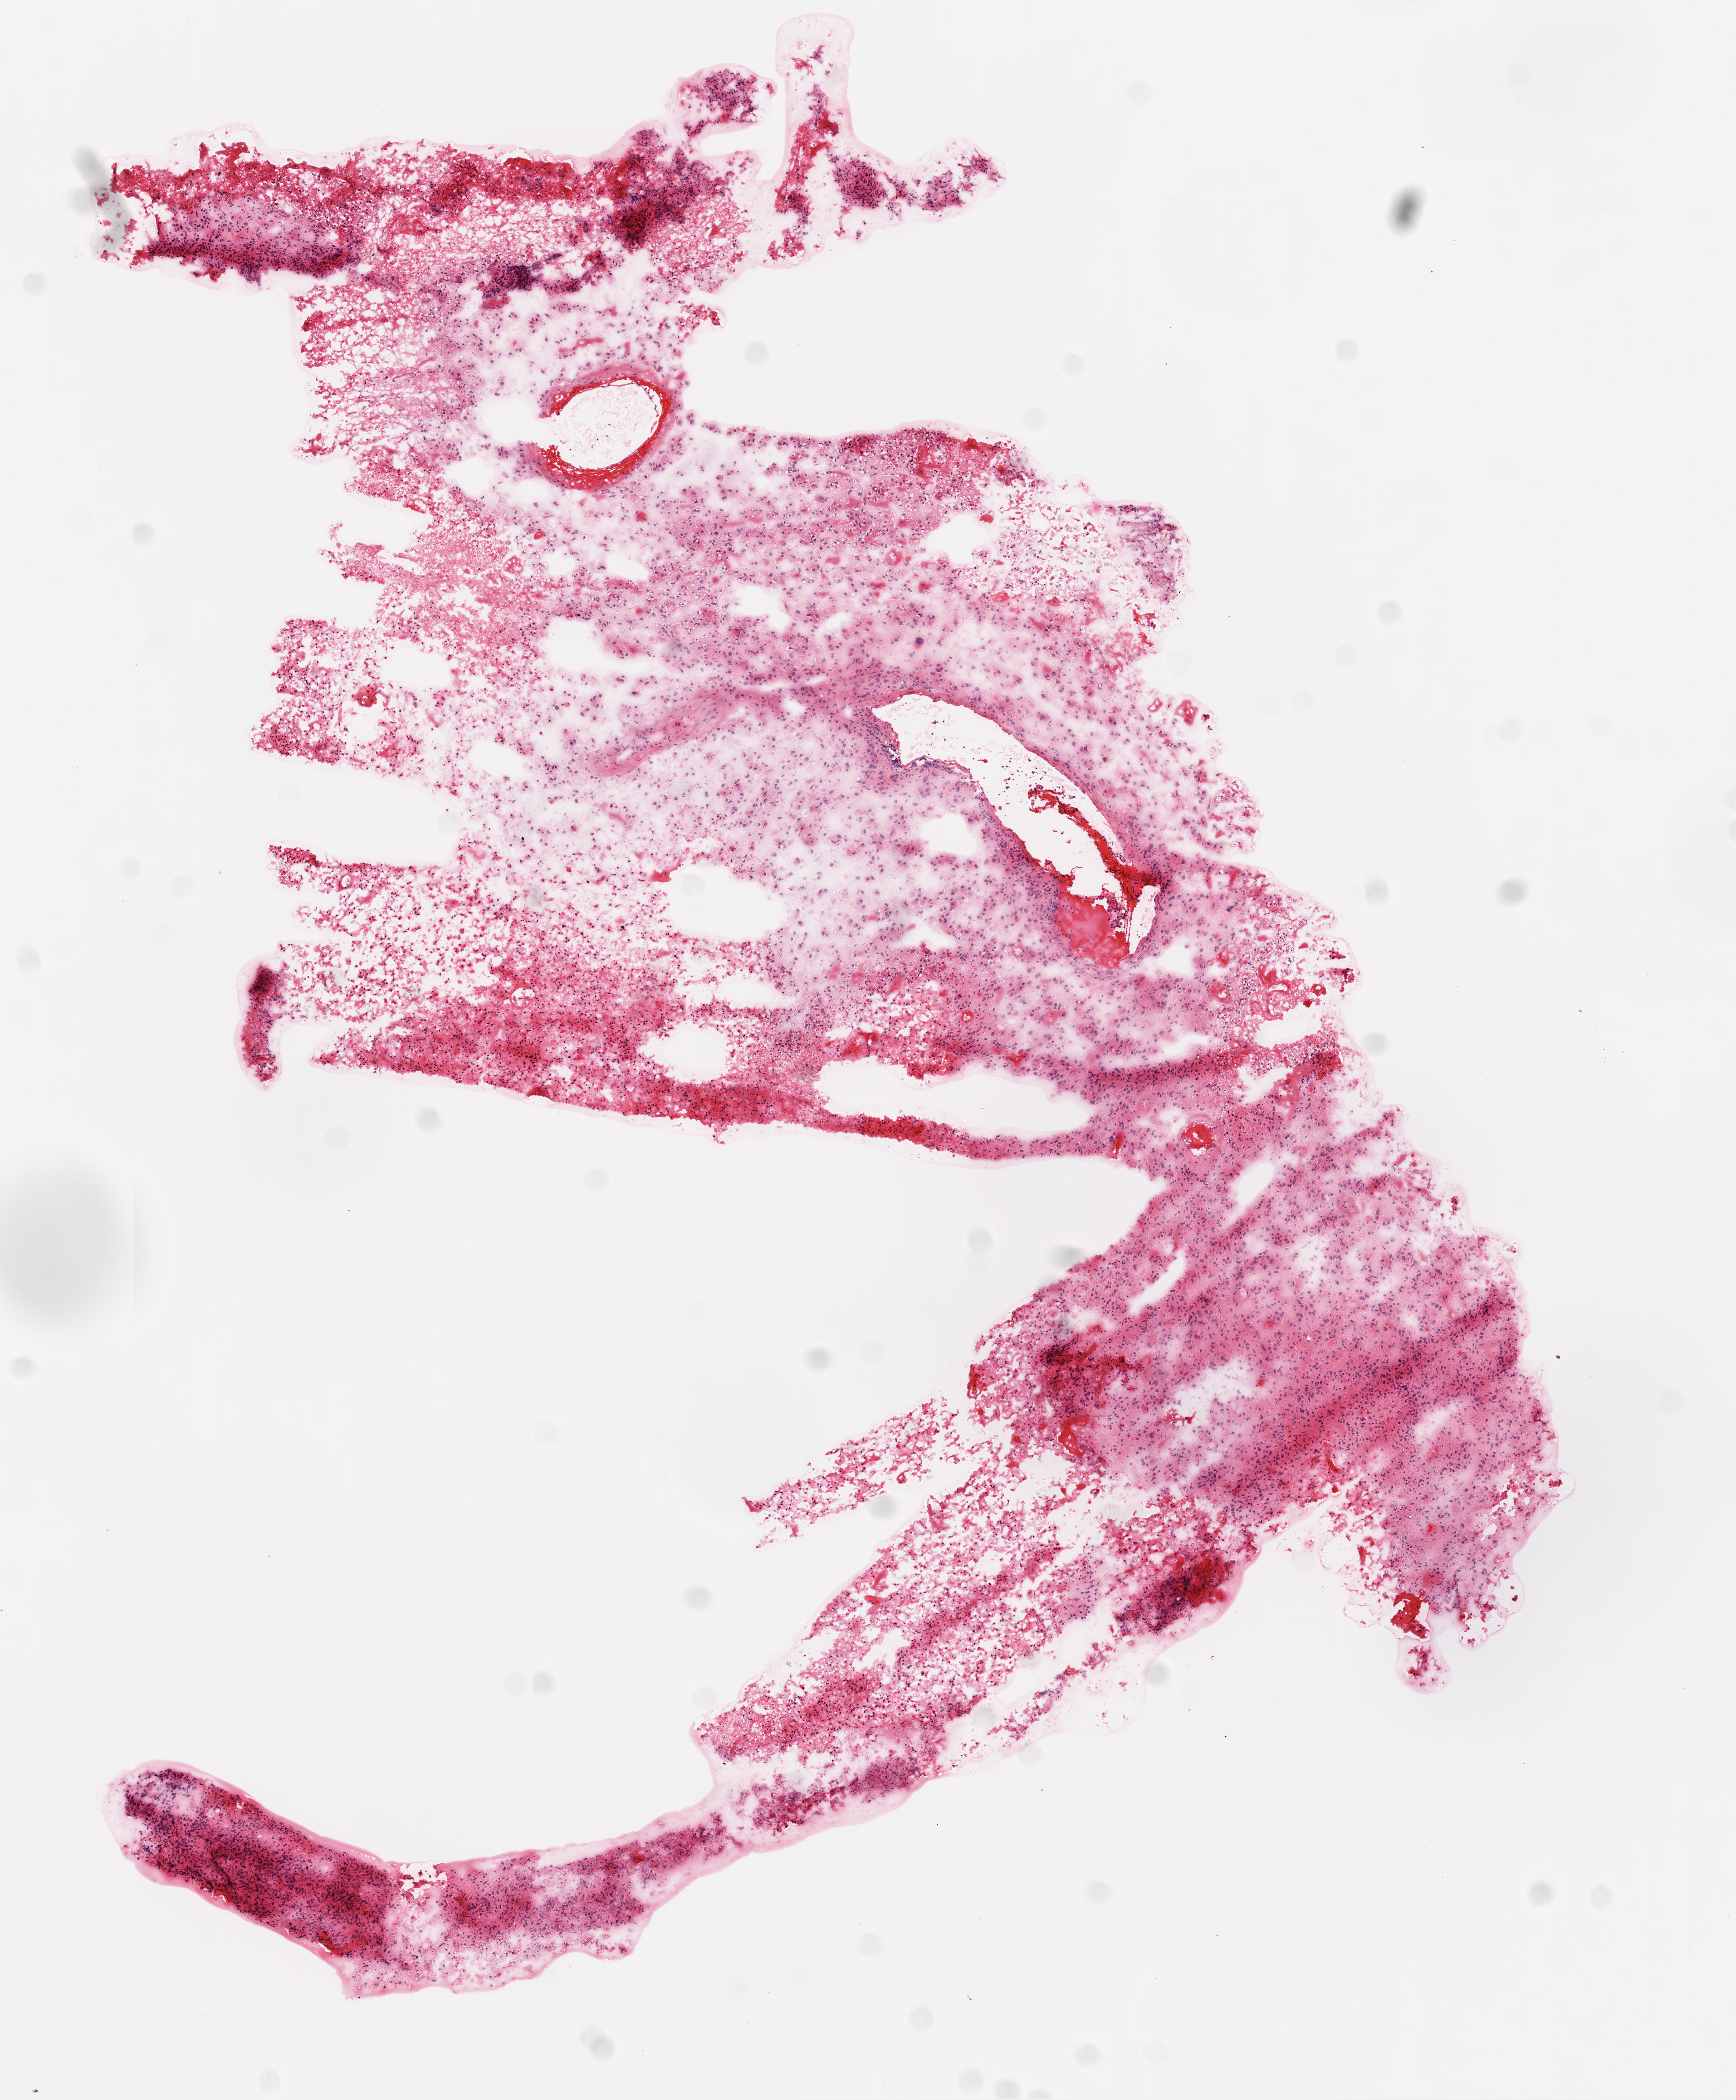
Hematoxylin and eosin (H&E) stained whole-slide image, shown as a low-resolution overview of the whole scanned area (about 6.3 x 7.6 mm); frozen section from the bottom of the tissue portion; primary tumour sample from the brain. Female patient; age at initial diagnosis 57 years. Slide review estimates, as recorded: tumour cells 70%, tumour nuclei 85%, normal cells 0%, stromal cells 10%, necrosis 20%.
- diagnosis: Glioblastoma